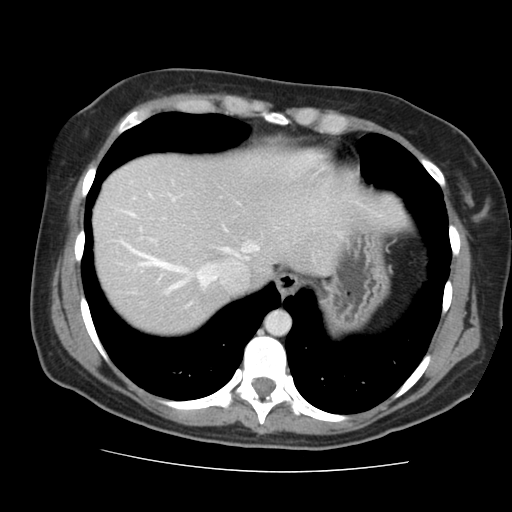
Contrast-enhanced abdominal CT, one axial slice. Position 128 of 144 along the scan axis. 120 kVp. Intravenous contrast given. Soft-tissue window (W 400 / L 40 HU). 2.5 mm slice thickness. 512 × 512 image matrix, field of view 333 × 333 mm. Female patient, age 46 years. From the clinical record (not read from this slice): diagnosis: colorectal cancer liver metastases, imaged before liver resection; multiple liver metastases: no; largest metastasis: 2.8 cm.
Structures marked on this image (manually delineated by an expert):
- hepatic veins: bounding box (x1, y1, x2, y2) in pixels: (128, 213, 258, 292)
- liver: (94, 149, 342, 334)
- planned liver remnant (the part of the liver to remain after resection): (94, 149, 342, 334)
- portal vein (with intrahepatic branches): (127, 246, 169, 266)